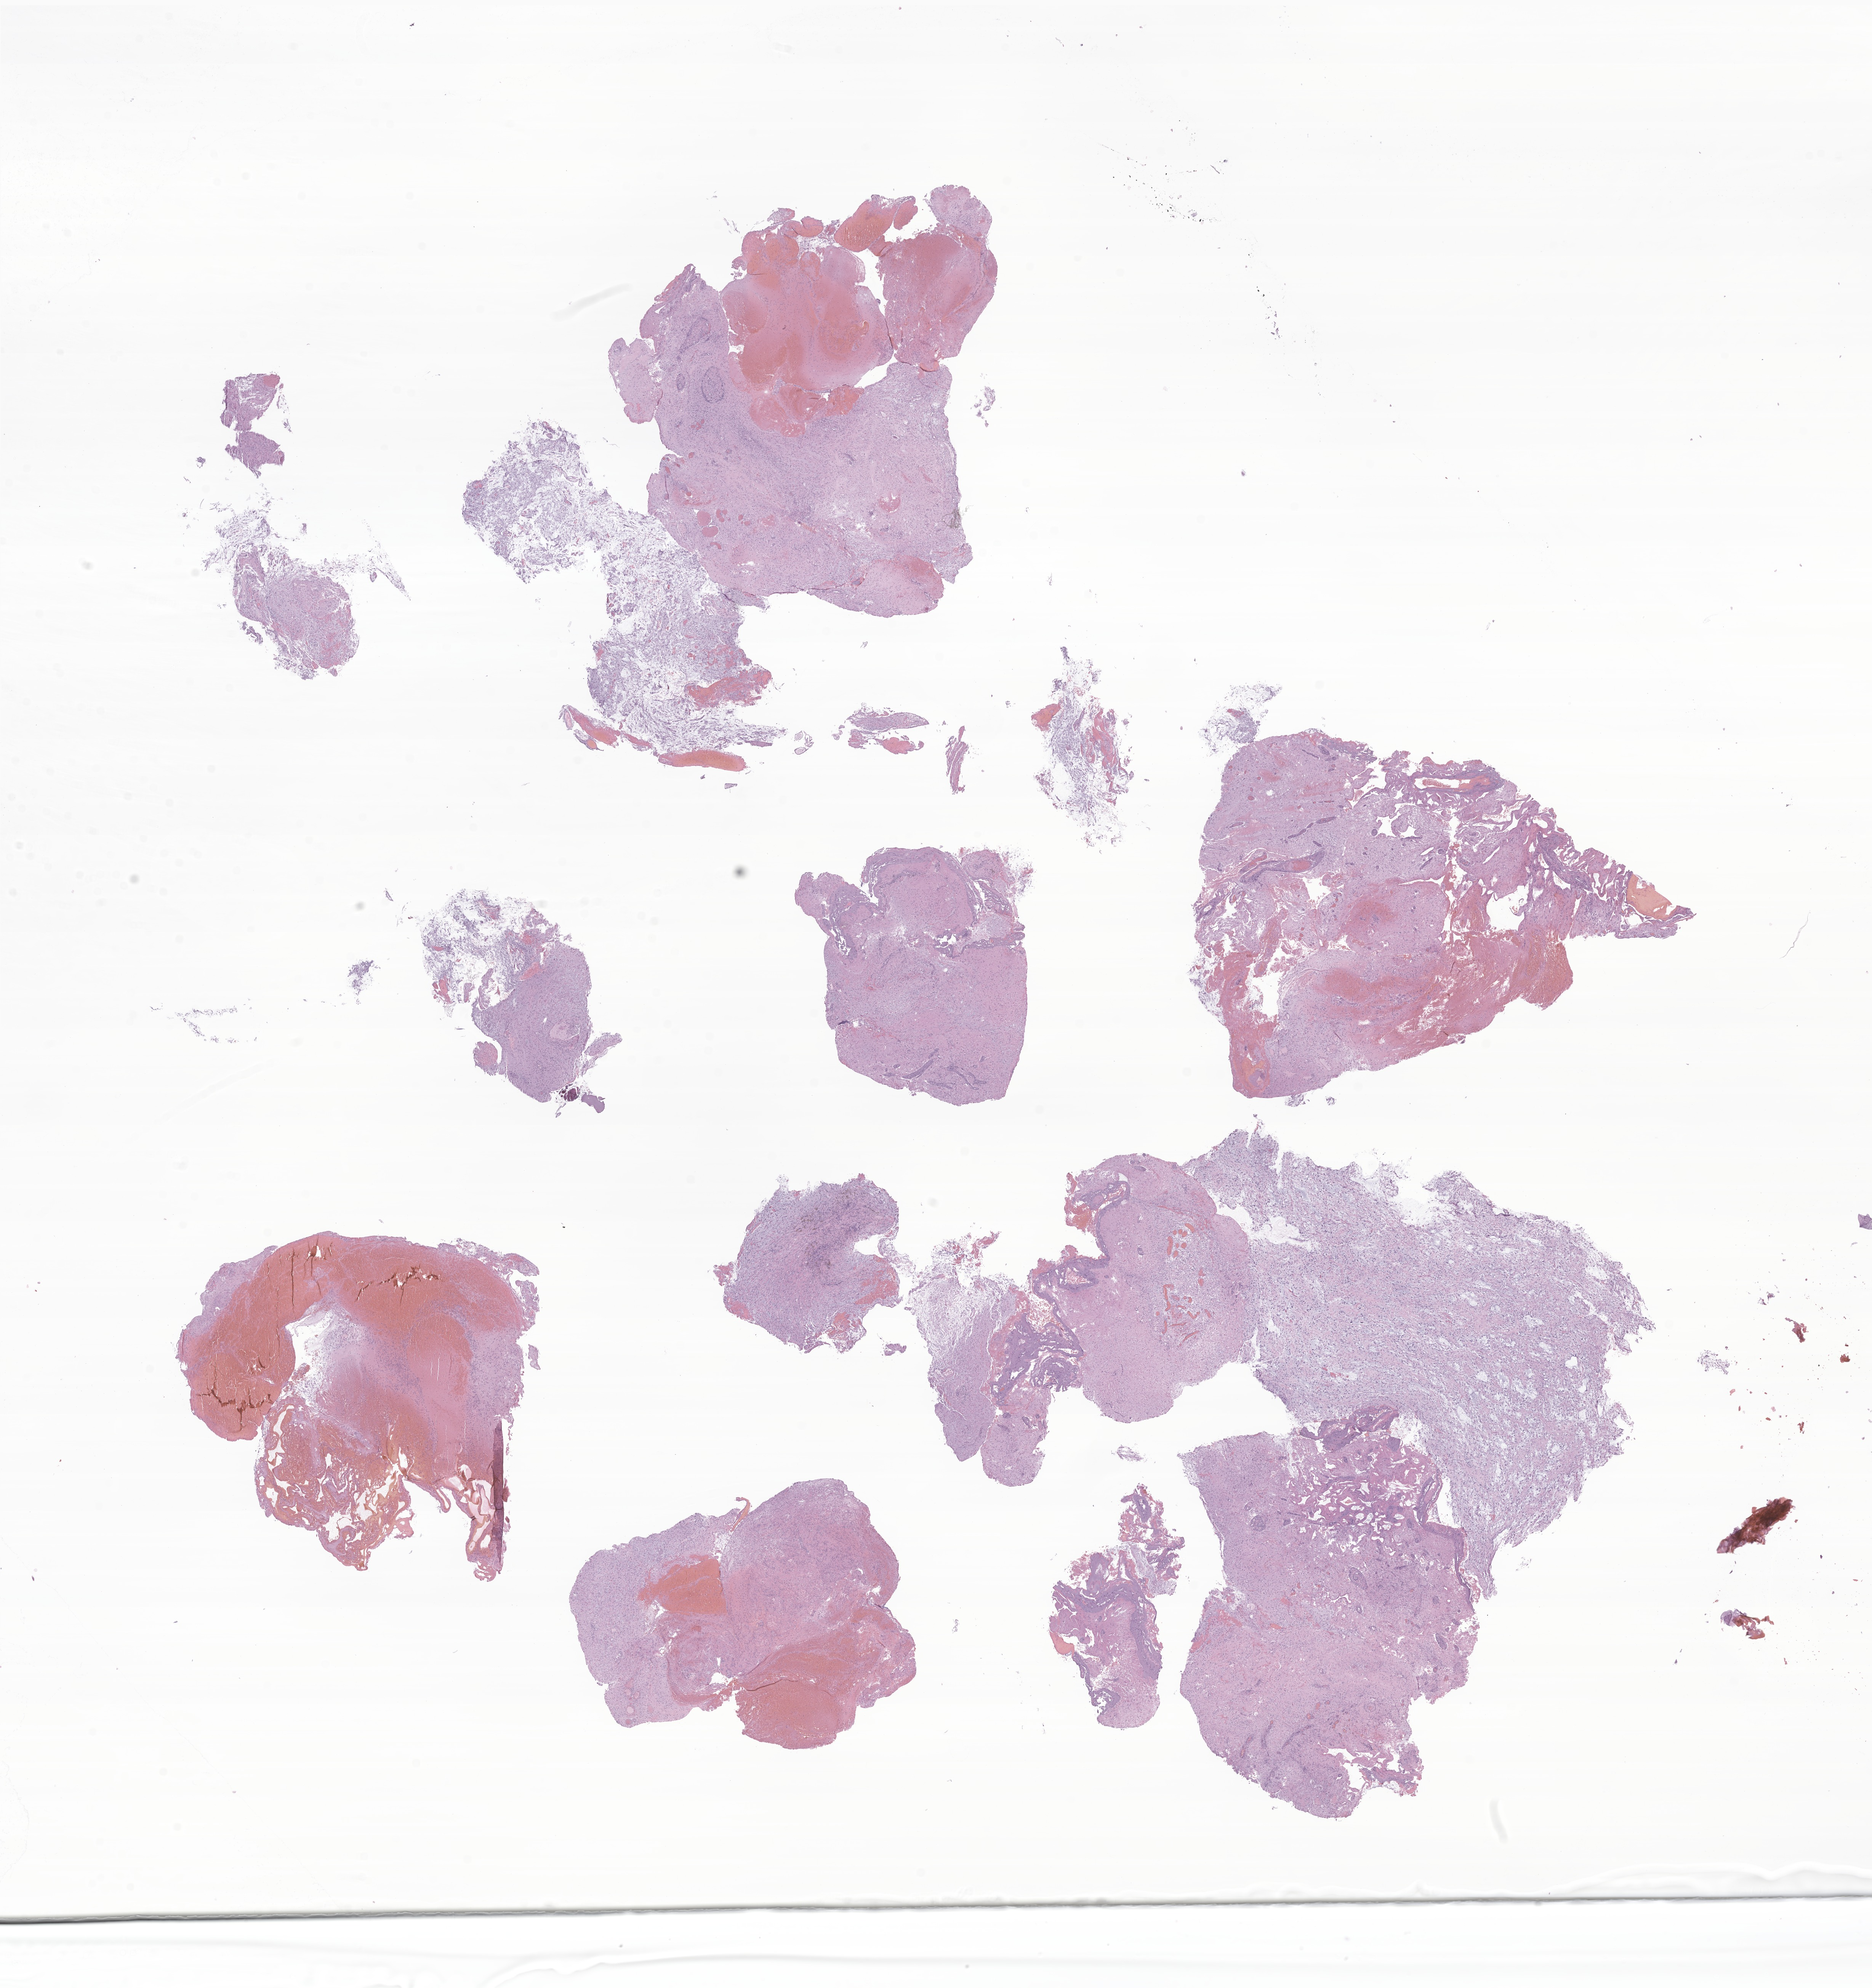
Digitized haematoxylin and eosin-stained section of tumor tissue from the brain — low-resolution overview of the scanned area, about 20.7 x 22.0 mm, formalin-fixed paraffin-embedded section. Patient female; age 173 months (14 years 5 months).
Diagnosis: Pilocytic astrocytoma.